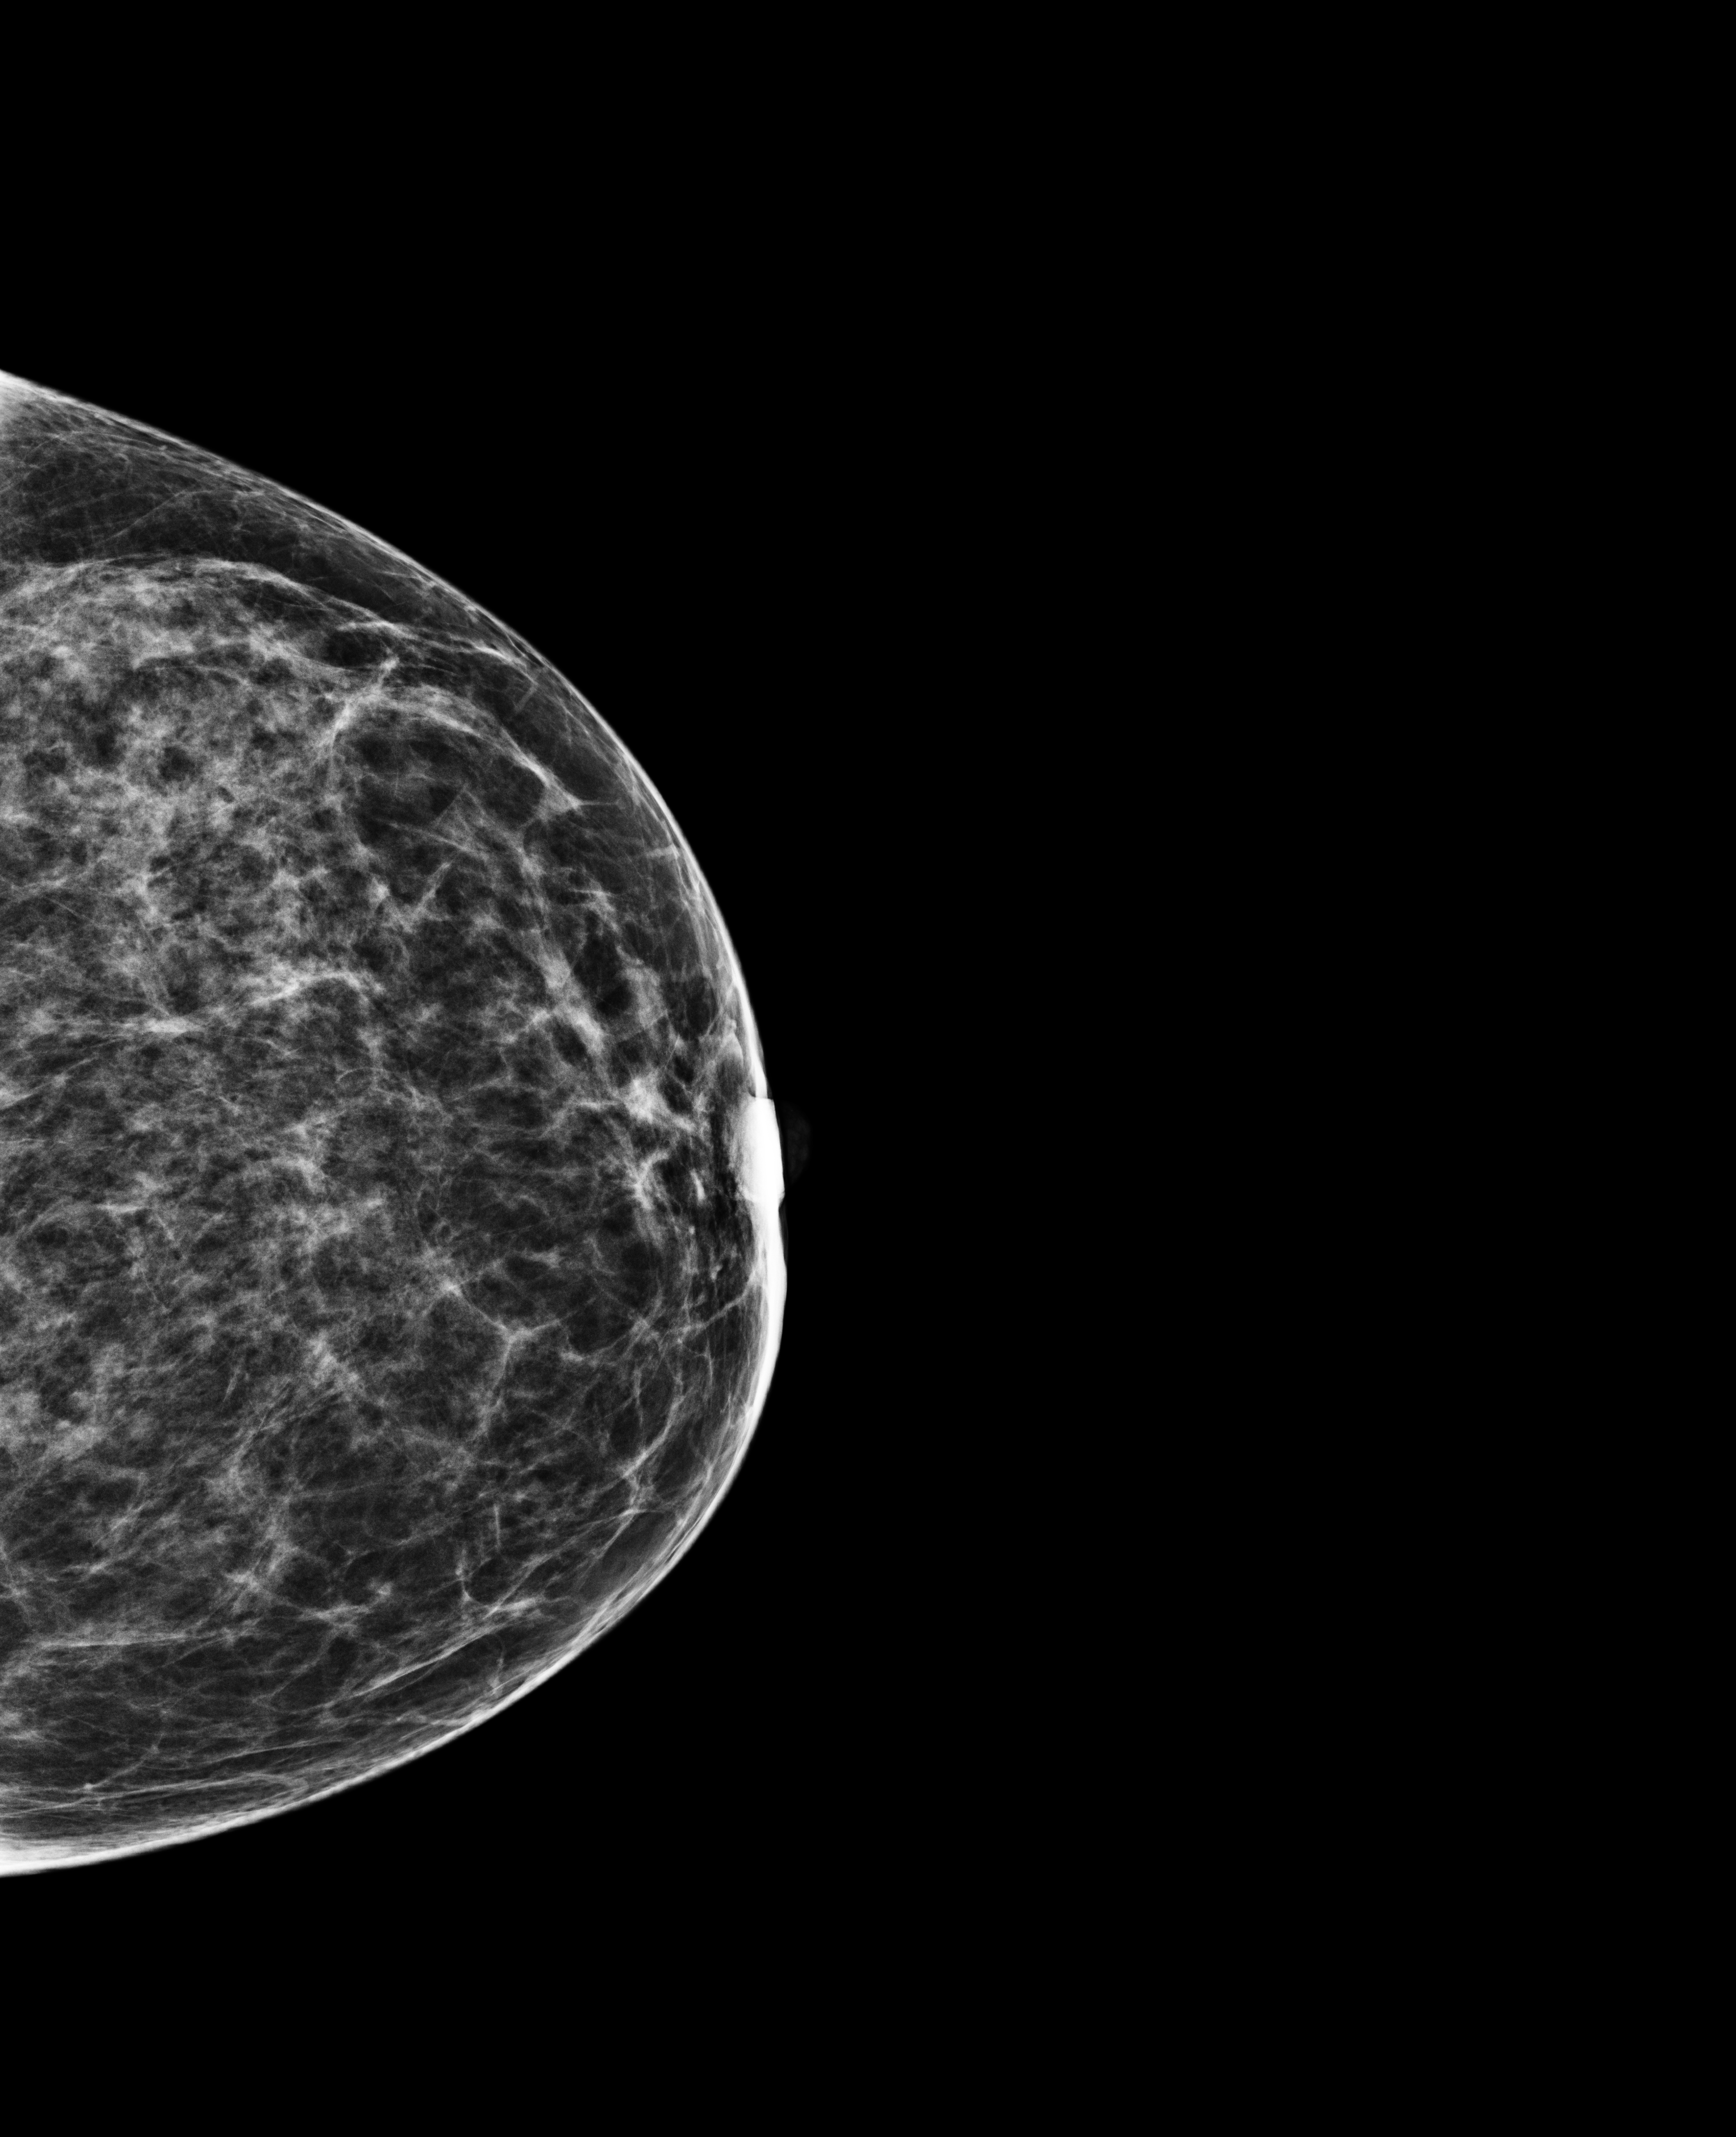
Annual screening mammography examination, compressed breast thickness 50 mm.
Image type: full-field digital mammogram. Breast: left. Projection: craniocaudal (CC) view.